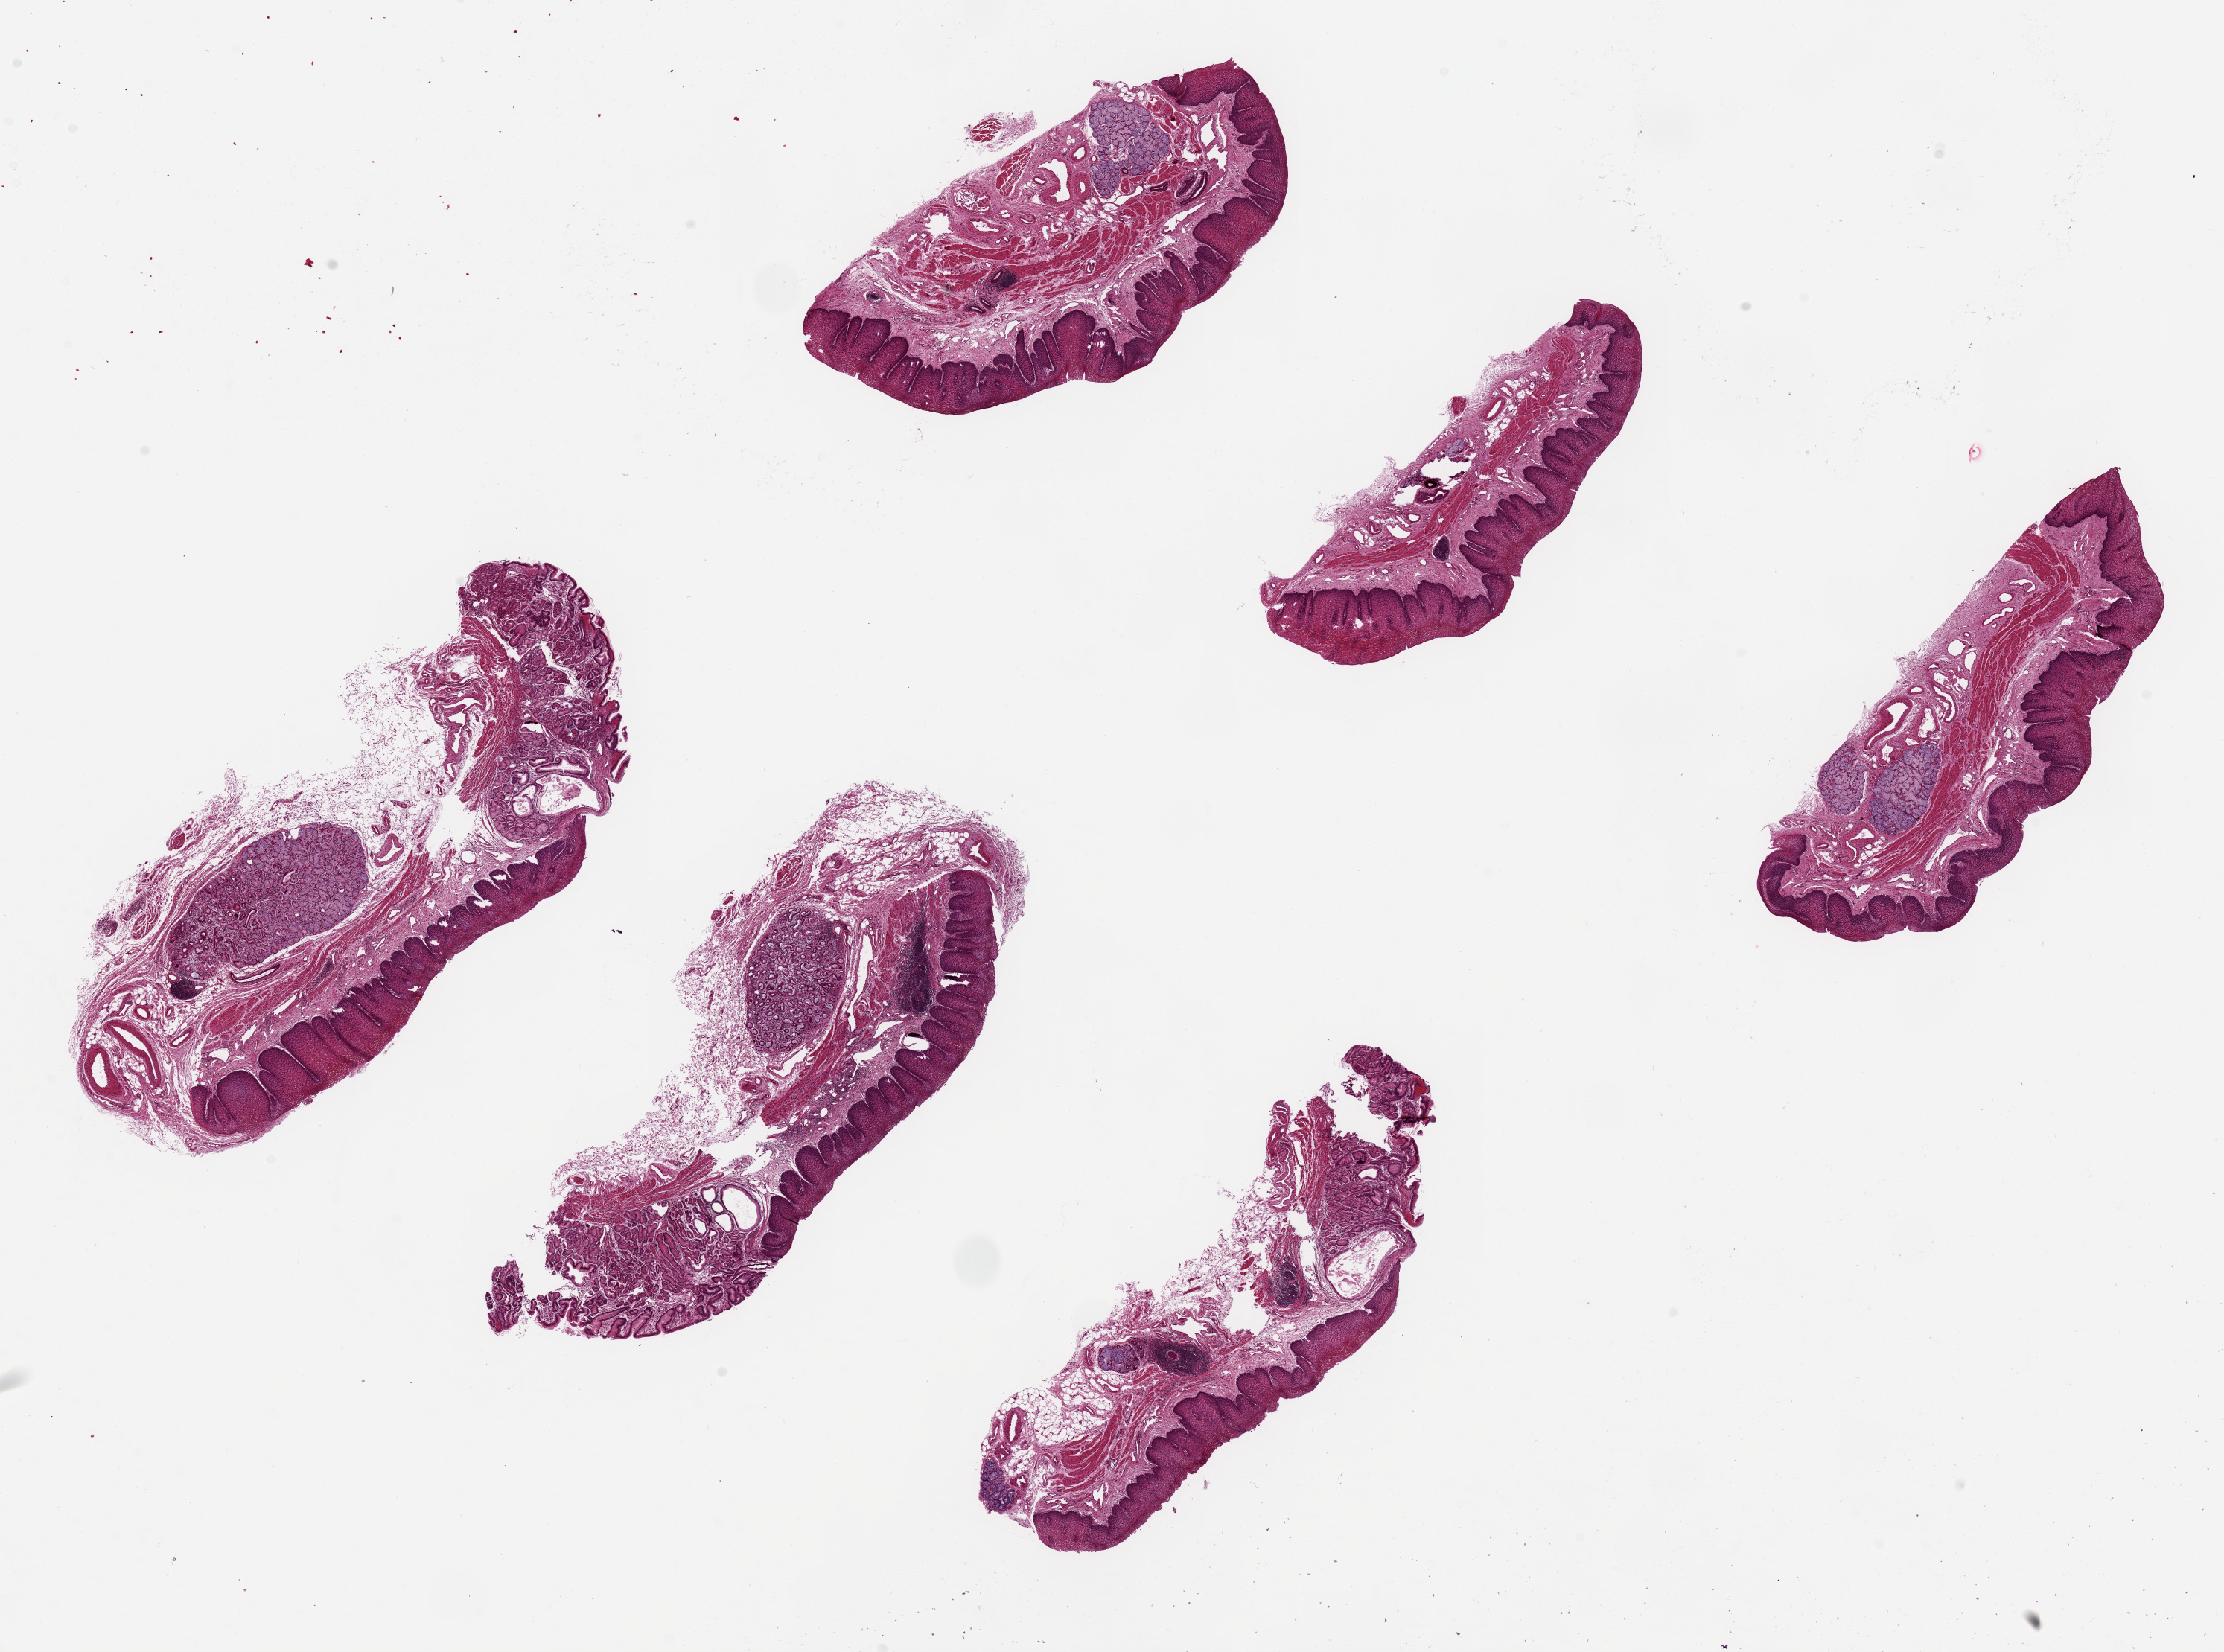
Digitized hematoxylin and eosin (H&E)-stained section, whole scanned area (about 23.6 x 17.6 mm) shown as a low-resolution overview. PAXgene-fixed, paraffin-embedded tissue. Sampled site (target tissue): esophageal mucous membrane. Tissue donor sample.
• reviewer comment on this tissue sample: 6 pieces up to 7x3 mm; 3 have squamous mucosa; 3 have squamous and glandular (cardiac) mucosa; none have muscularis